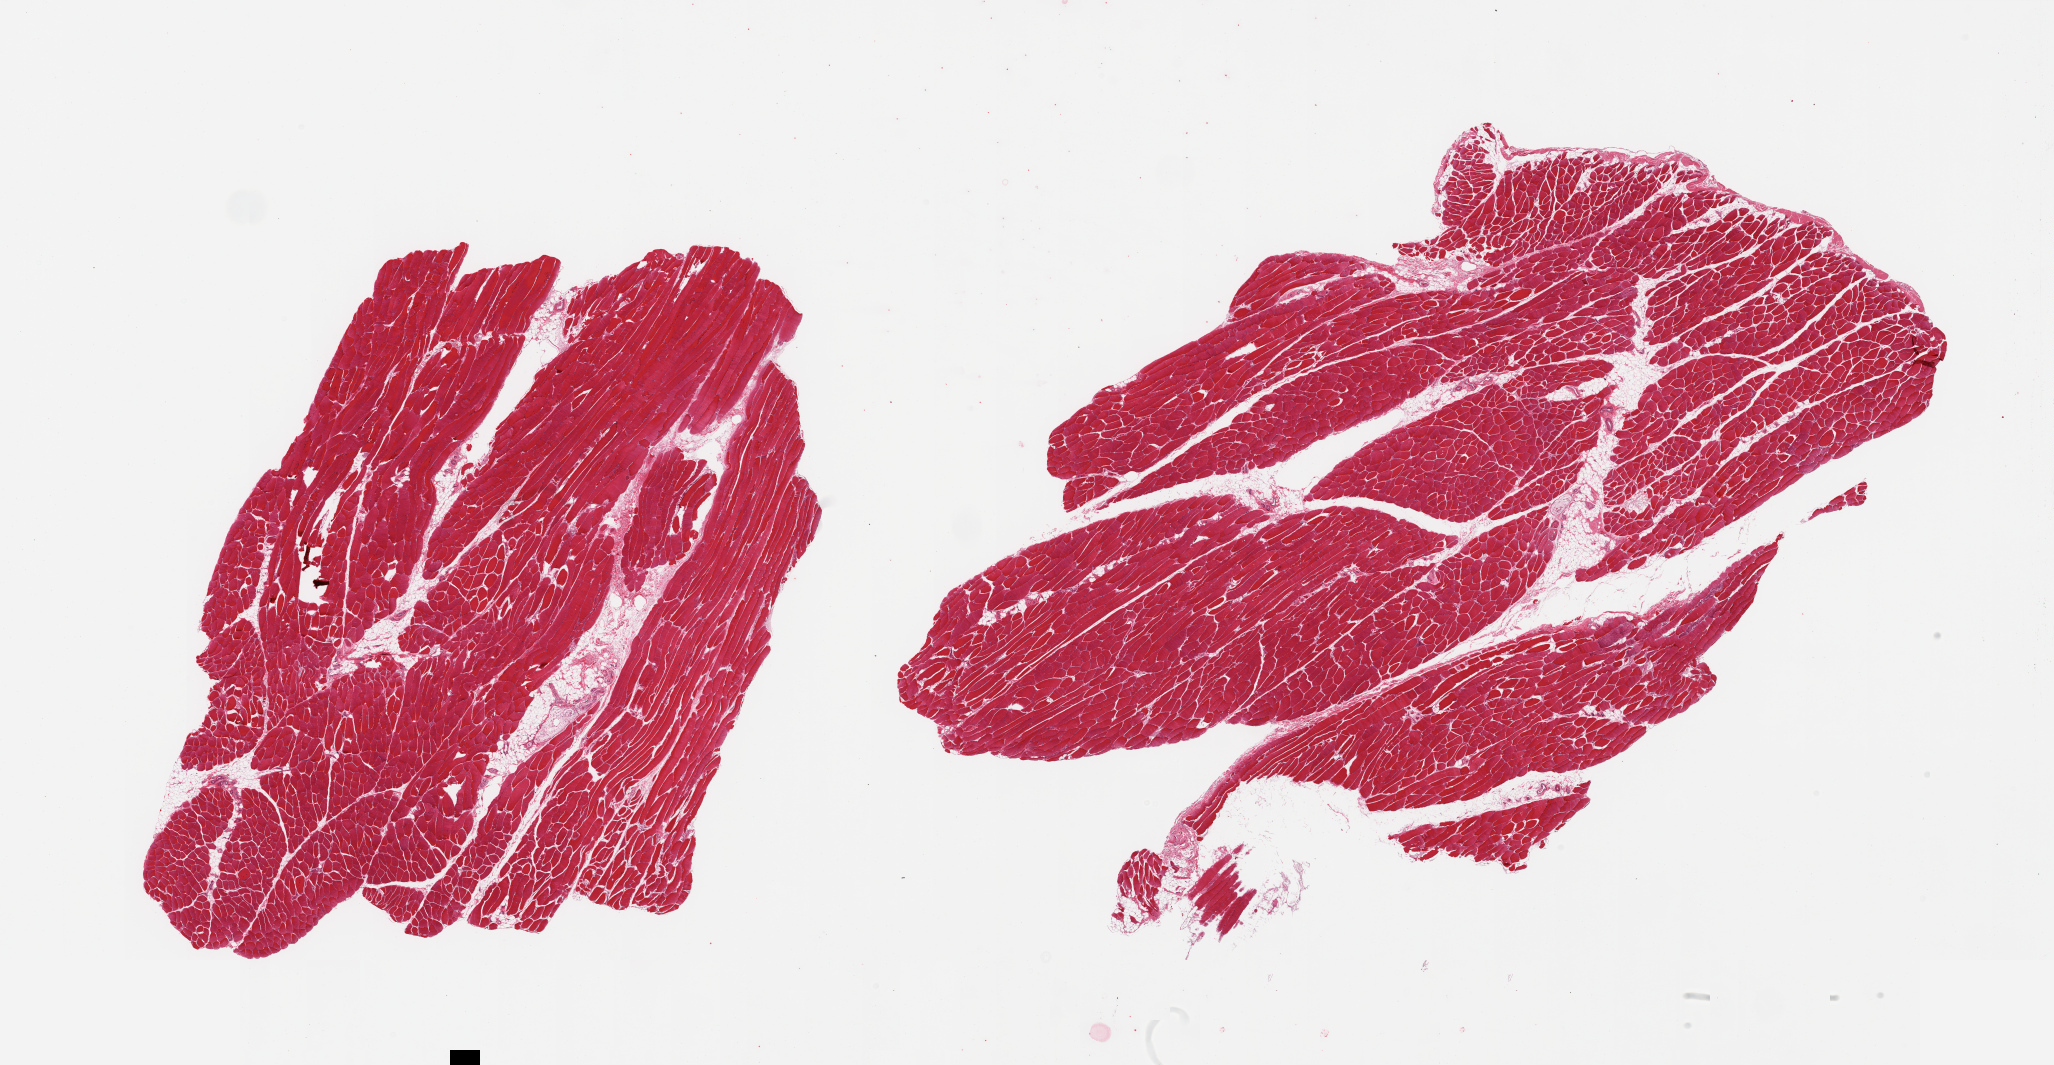
H&E whole-slide image — shown as a low-resolution overview of the whole scanned area (about 32.5 x 16.8 mm, acquisition: 20x scan); PAXgene-fixed paraffin-embedded (PFPE) section; target tissue: skeletal muscle; donor tissue sample. Male donor.
• review note (as recorded): 2 pieces; includes up to 10% internal fat